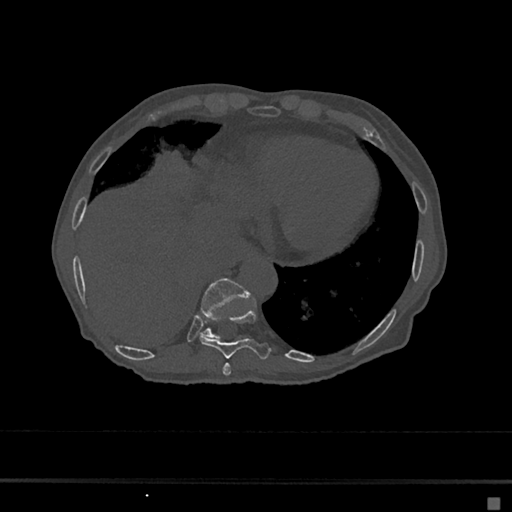
CT including the spine, one axial slice; position 260 of 797 along the scan axis; reconstruction kernel Br40s/3; 120 kVp; bone window (W 1800 / L 400 HU); 0.5 mm slice thickness; 512 × 512 image matrix. Patient: female, 68 years. From the clinical record (not read from this slice): primary cancer: renal.
Outlined on this slice (semi-automatic segmentation, software-assisted and operator-edited):
- T10 vertebra: box from (x=200, y=278) to (x=249, y=339) px
- T8 vertebra: (x=222, y=364)–(x=231, y=376)
- T9 vertebra: (x=200, y=308)–(x=271, y=360)